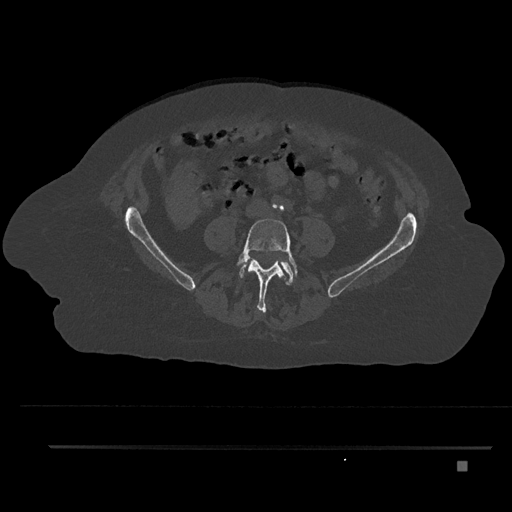
CT including the spine, one axial slice; position 76 of 797 along the scan axis; 120 kVp; bone window (W 1800 / L 400 HU); 512 × 512 image matrix, field of view 437 × 437 mm. Patient: female, 76 years. Case-level facts recorded for this patient, not image findings: primary cancer: lung.
Annotated regions visible in this slice (semi-automatically segmented with operator editing):
- L4 vertebra: box from (x=236, y=218) to (x=298, y=313) px
- L5 vertebra: (x=239, y=261)–(x=296, y=285)